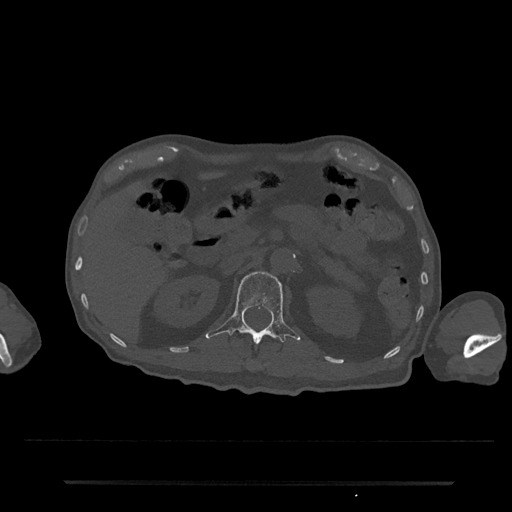
CT including the spine, one axial slice; slice 136 of 797 in the series (ordered by position); reconstruction kernel Br40s/3; 120 kVp; bone window (W 1800 / L 400 HU); 512 × 512 image matrix, field of view 427 × 427 mm. Patient: male, 74 years. Case-level facts recorded for this patient, not image findings: primary cancer: prostate.
Structures marked on this image (semi-automatic segmentation, software-assisted and operator-edited):
- L1 vertebra: bounding box (x1, y1, x2, y2) in pixels: (206, 271, 300, 344)